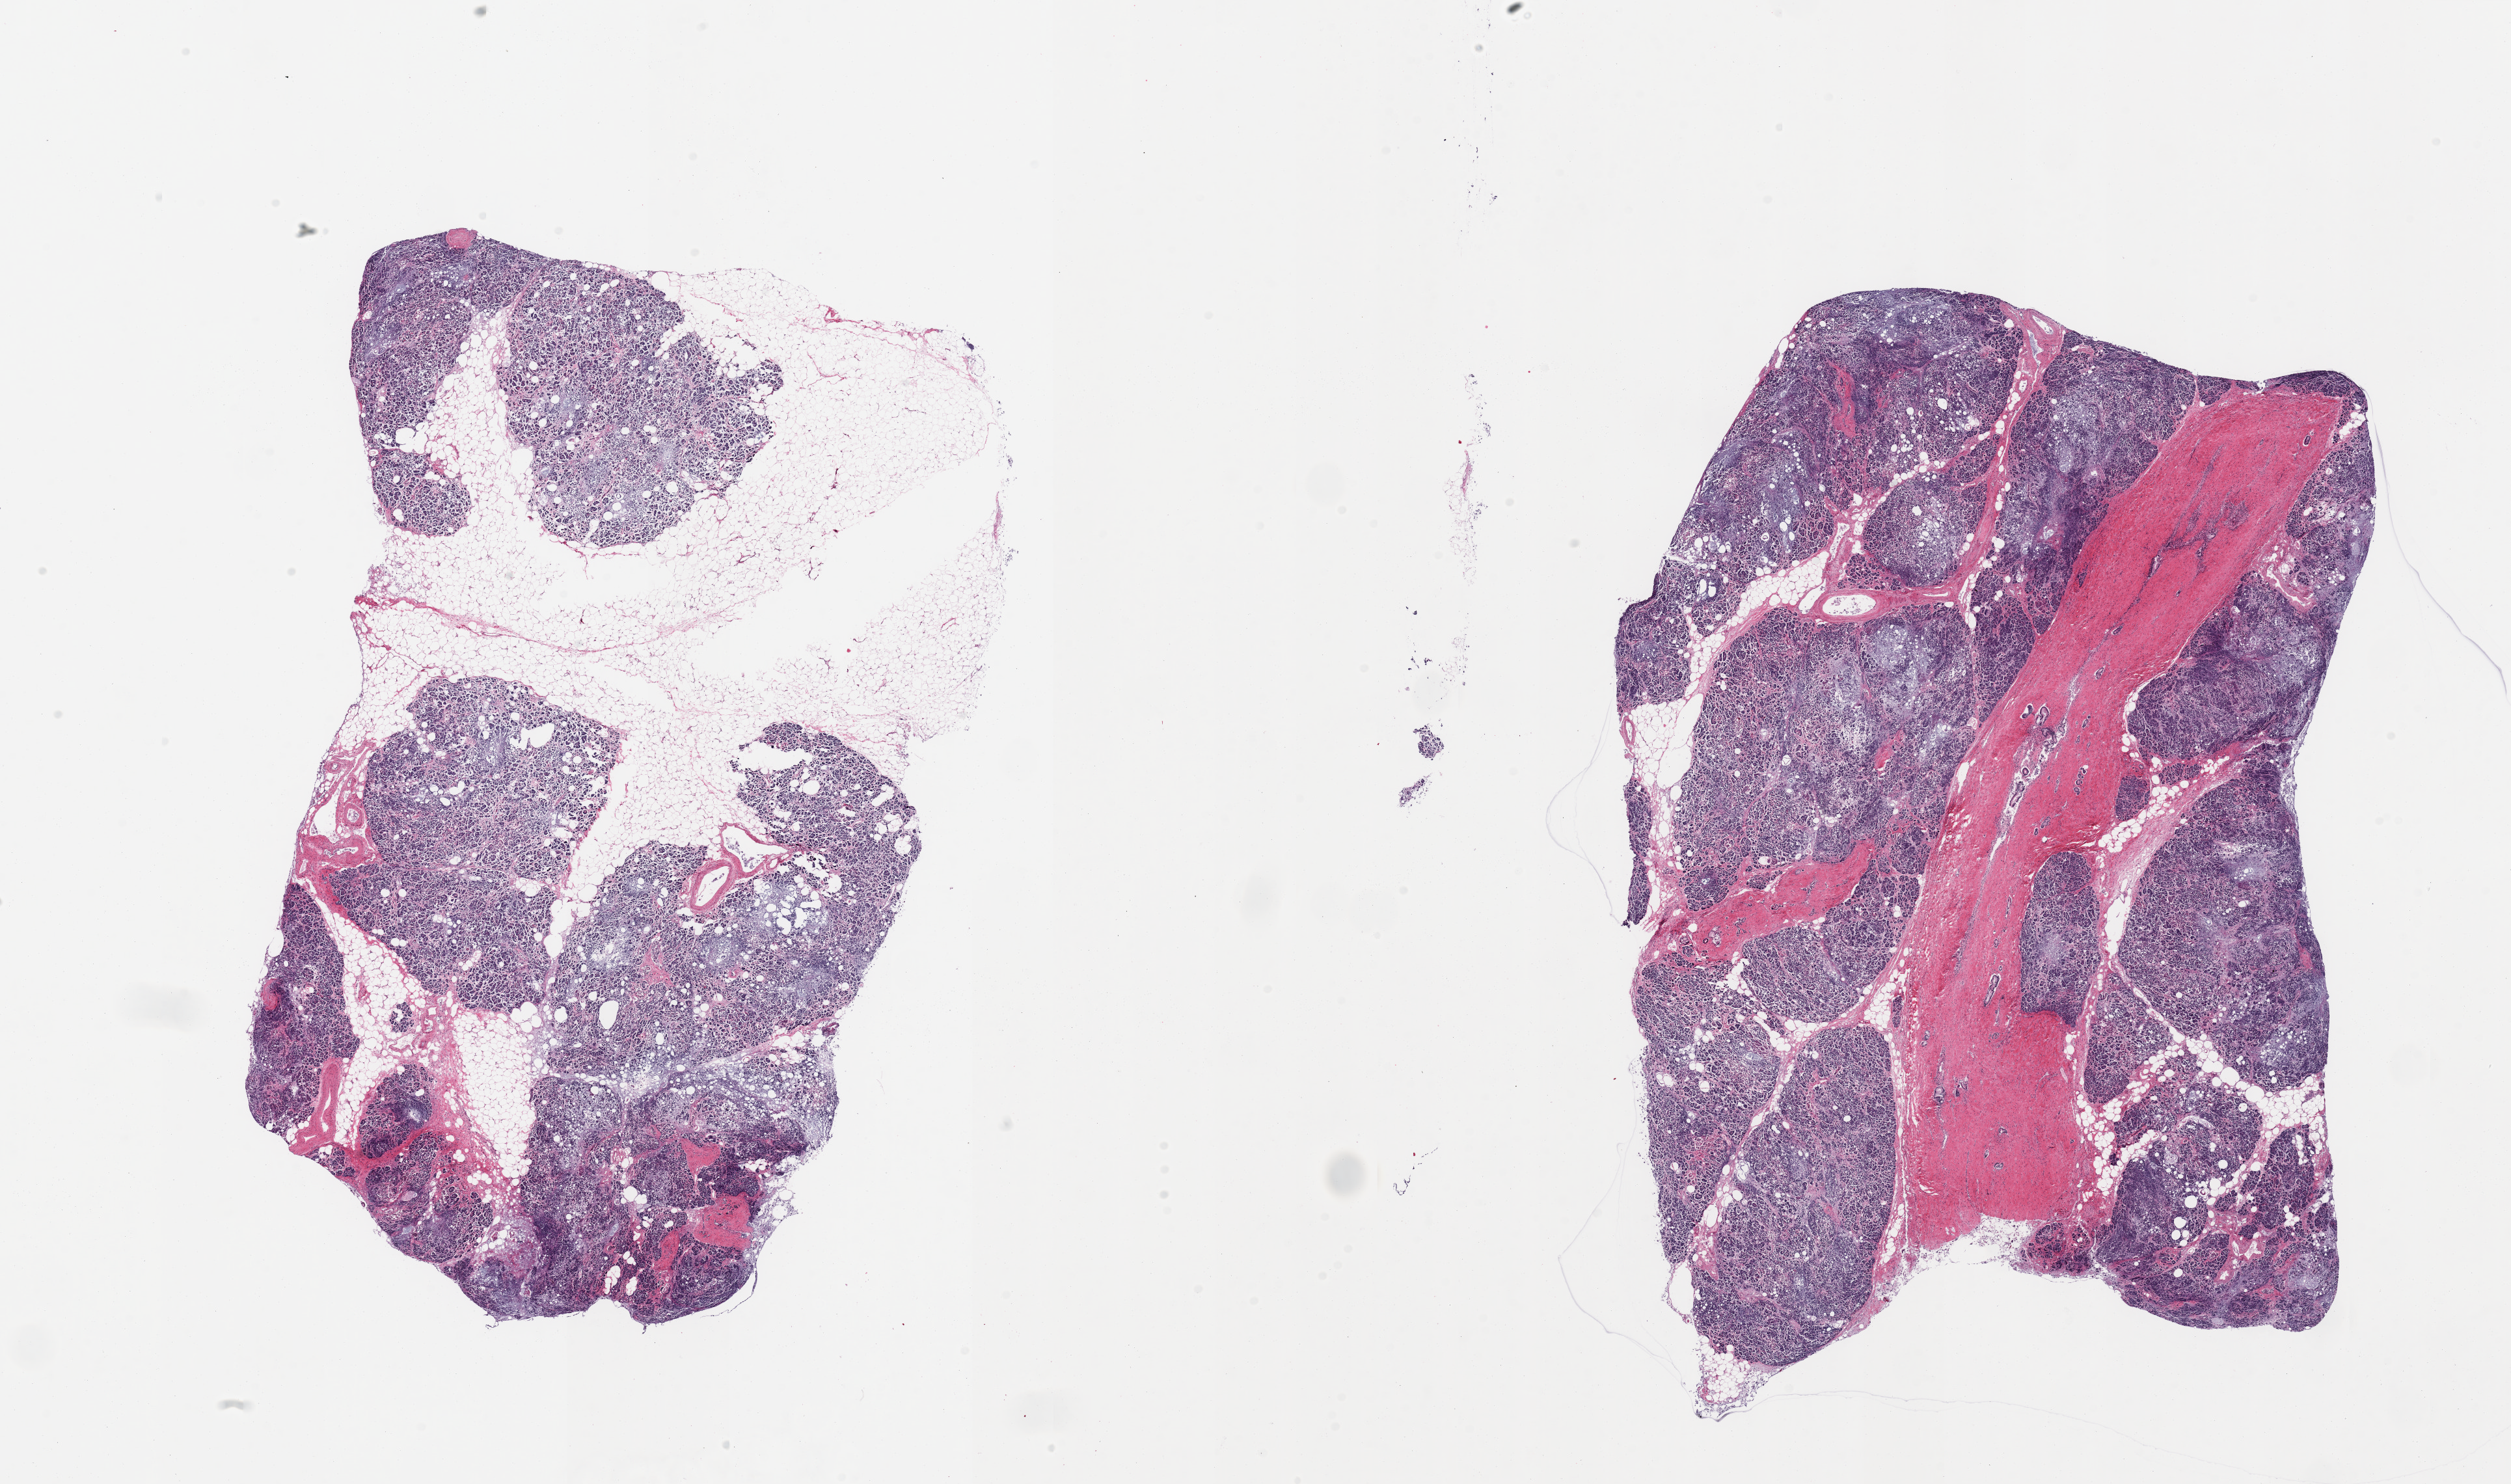
Digitized H&E-stained section, shown as a low-resolution overview of the whole scanned area (about 30.5 x 18.0 mm). PAXgene-fixed, paraffin-embedded tissue. Target tissue: pancreas. Donor tissue sample.
Review note (as recorded): 2 pieces; some moderate but mostly severe parenchymal autolysis; 50% internal/external fat and wide fibrous band.